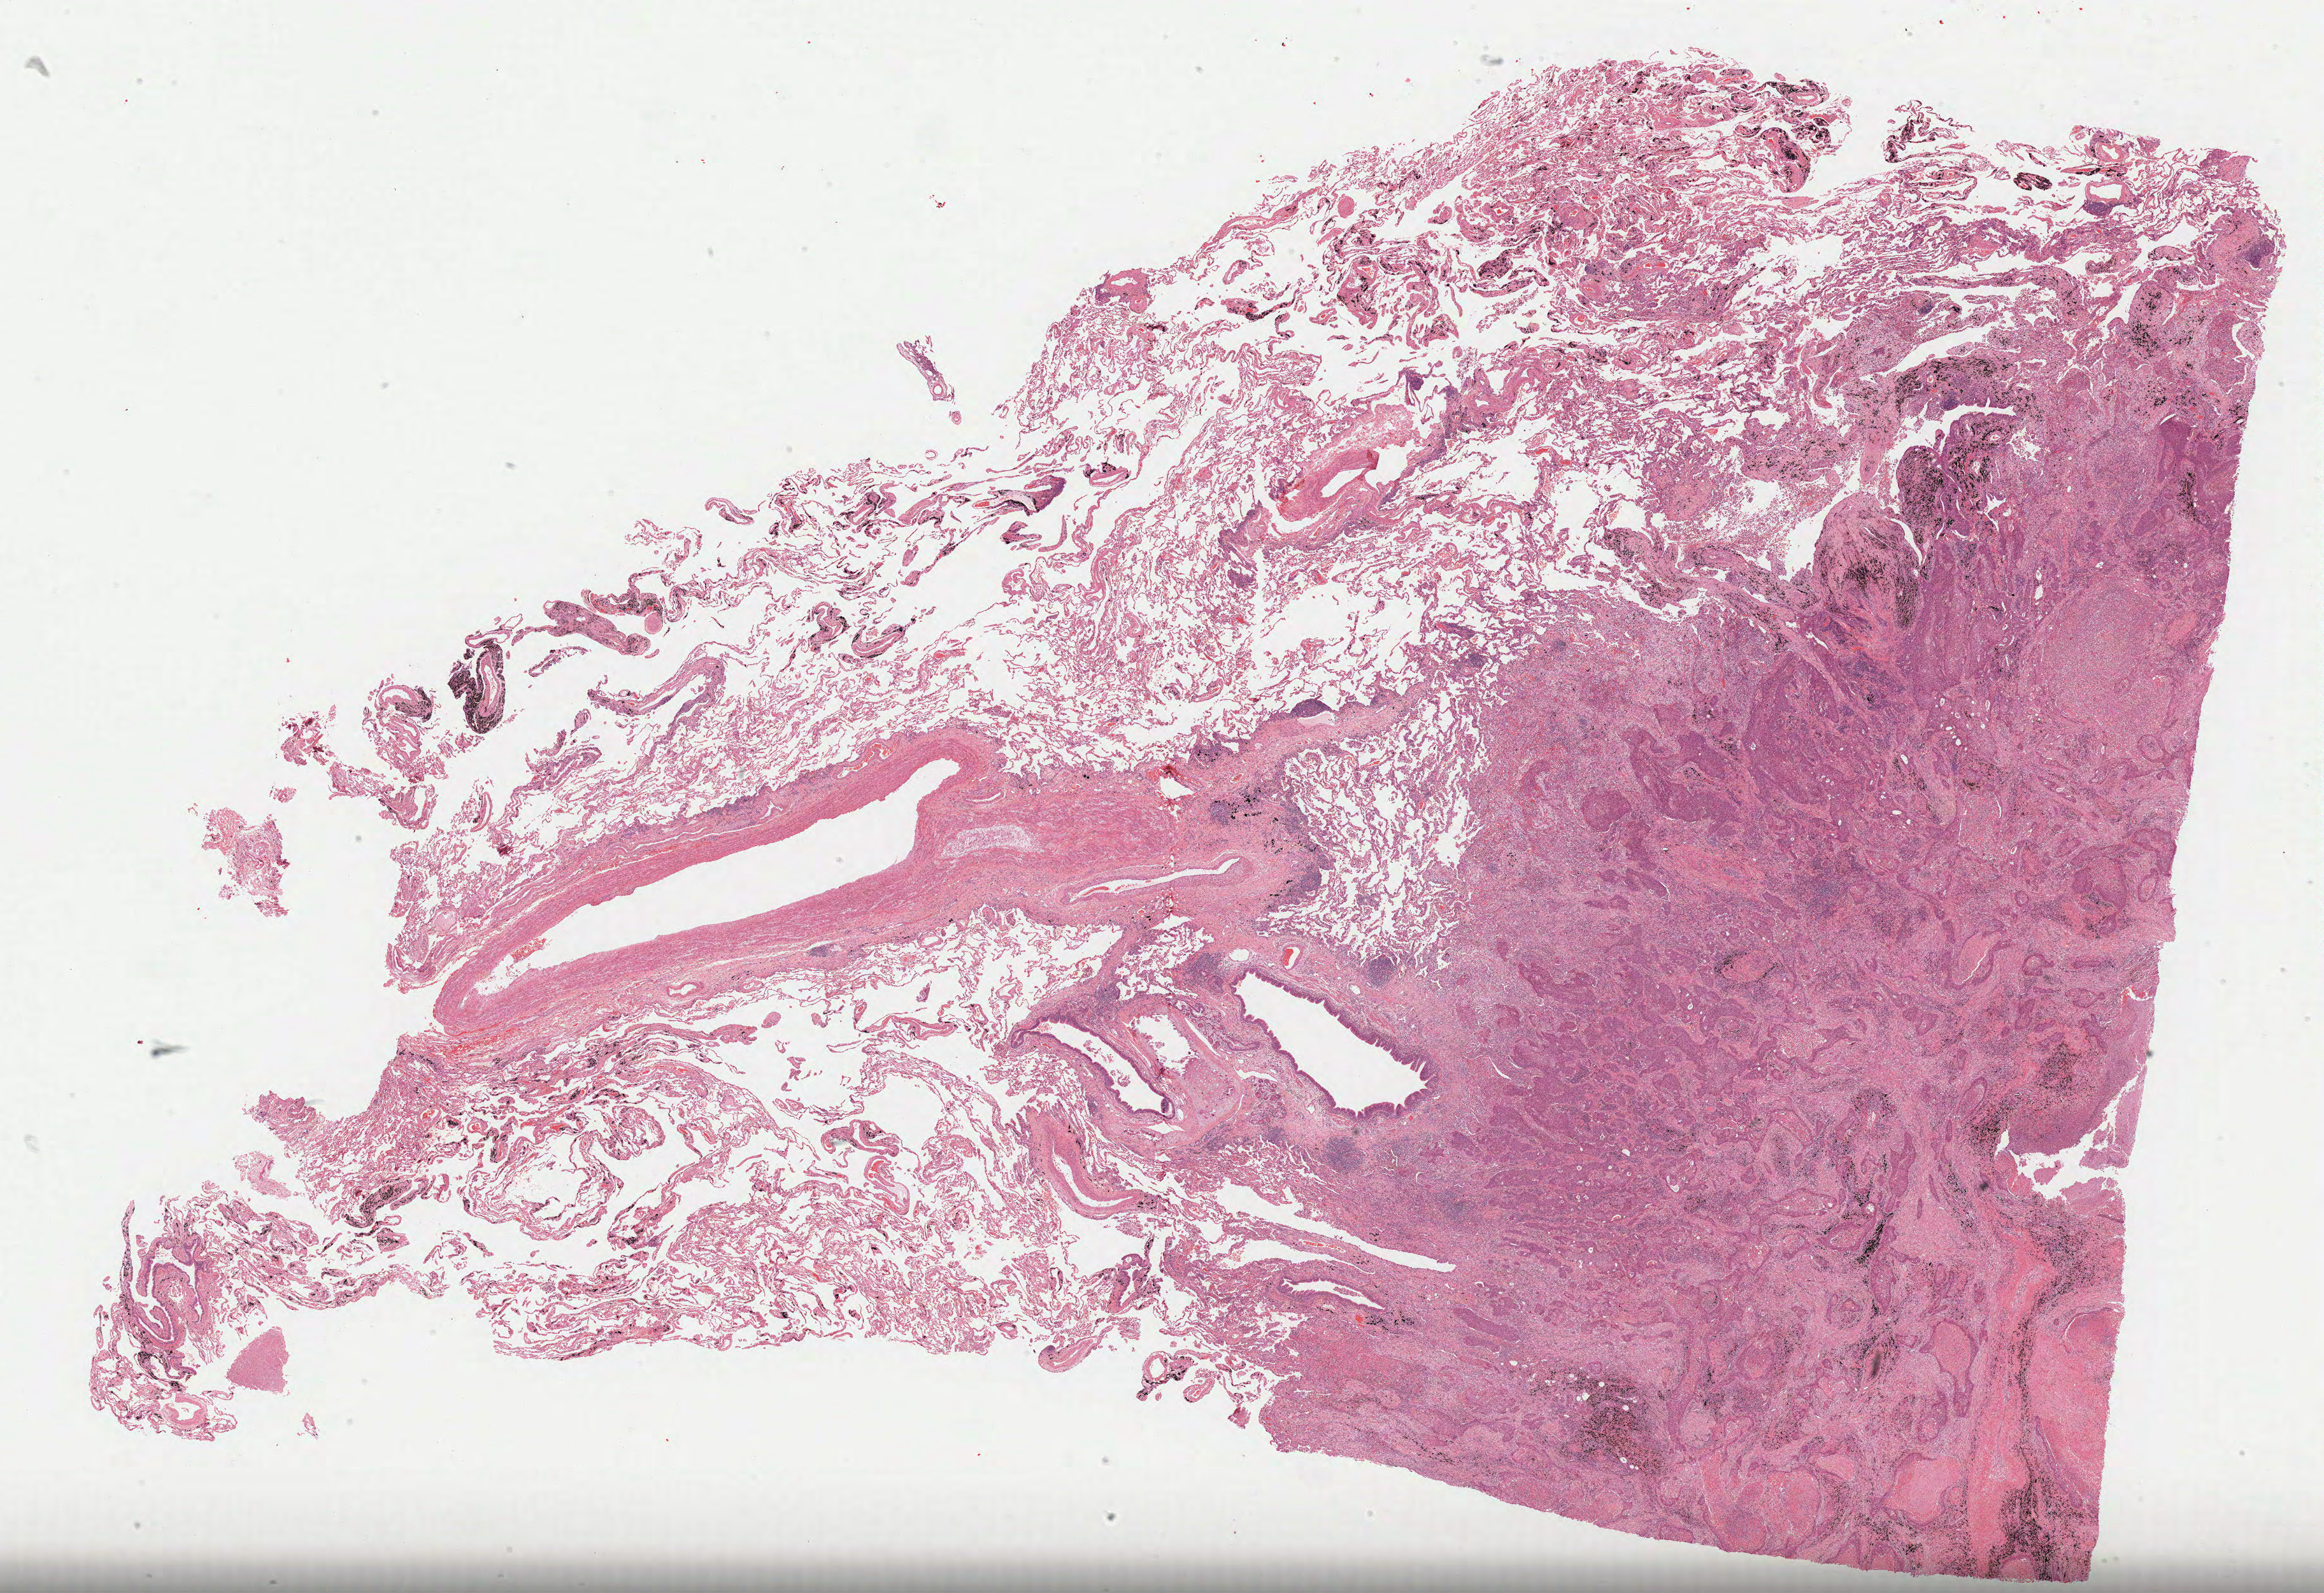
Whole-slide histology image, Hematoxylin and eosin (H&E) stained — a low-resolution overview of the entire scanned area, about 29.4 x 20.2 mm (acquisition: 40x scan), FFPE section, lung, primary tumour sample. Male patient; age at initial diagnosis 72 years.
Laterality: left. Diagnosis: Squamous cell carcinoma, NOS (upper lobe, lung). AJCC pathologic stage: IB.